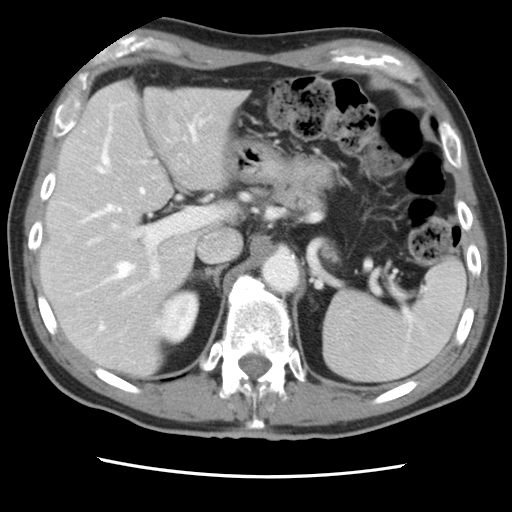
Contrast-enhanced abdominal CT, one axial slice. 120 kVp. Intravenous contrast given. Soft-tissue window (W 400 / L 40 HU). 5 mm slice thickness. 512 × 512 image matrix. Male patient, age 69 years. From the clinical record (not read from this slice): diagnosis: colorectal cancer liver metastases, imaged before liver resection; multiple liver metastases: yes; largest metastasis: 3.5 cm; disease in both lobes: no.
Annotated regions visible in this slice (expert manual segmentation):
- hepatic veins: bounding box (x1, y1, x2, y2) in pixels: (87, 126, 196, 330)
- liver: (42, 82, 244, 377)
- planned liver remnant (the part of the liver to remain after resection): (42, 139, 200, 377)
- portal vein (with intrahepatic branches): (87, 122, 218, 297)